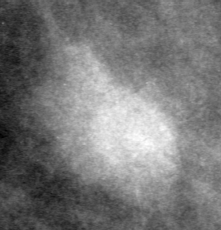
Cropped region of a digitized screen-film mammogram centred on a radiologist-marked abnormality; left breast; CC view.
Marked abnormality: mass, shape irregular, margins ill defined; BI-RADS assessment category 4; pathology (as recorded): benign.